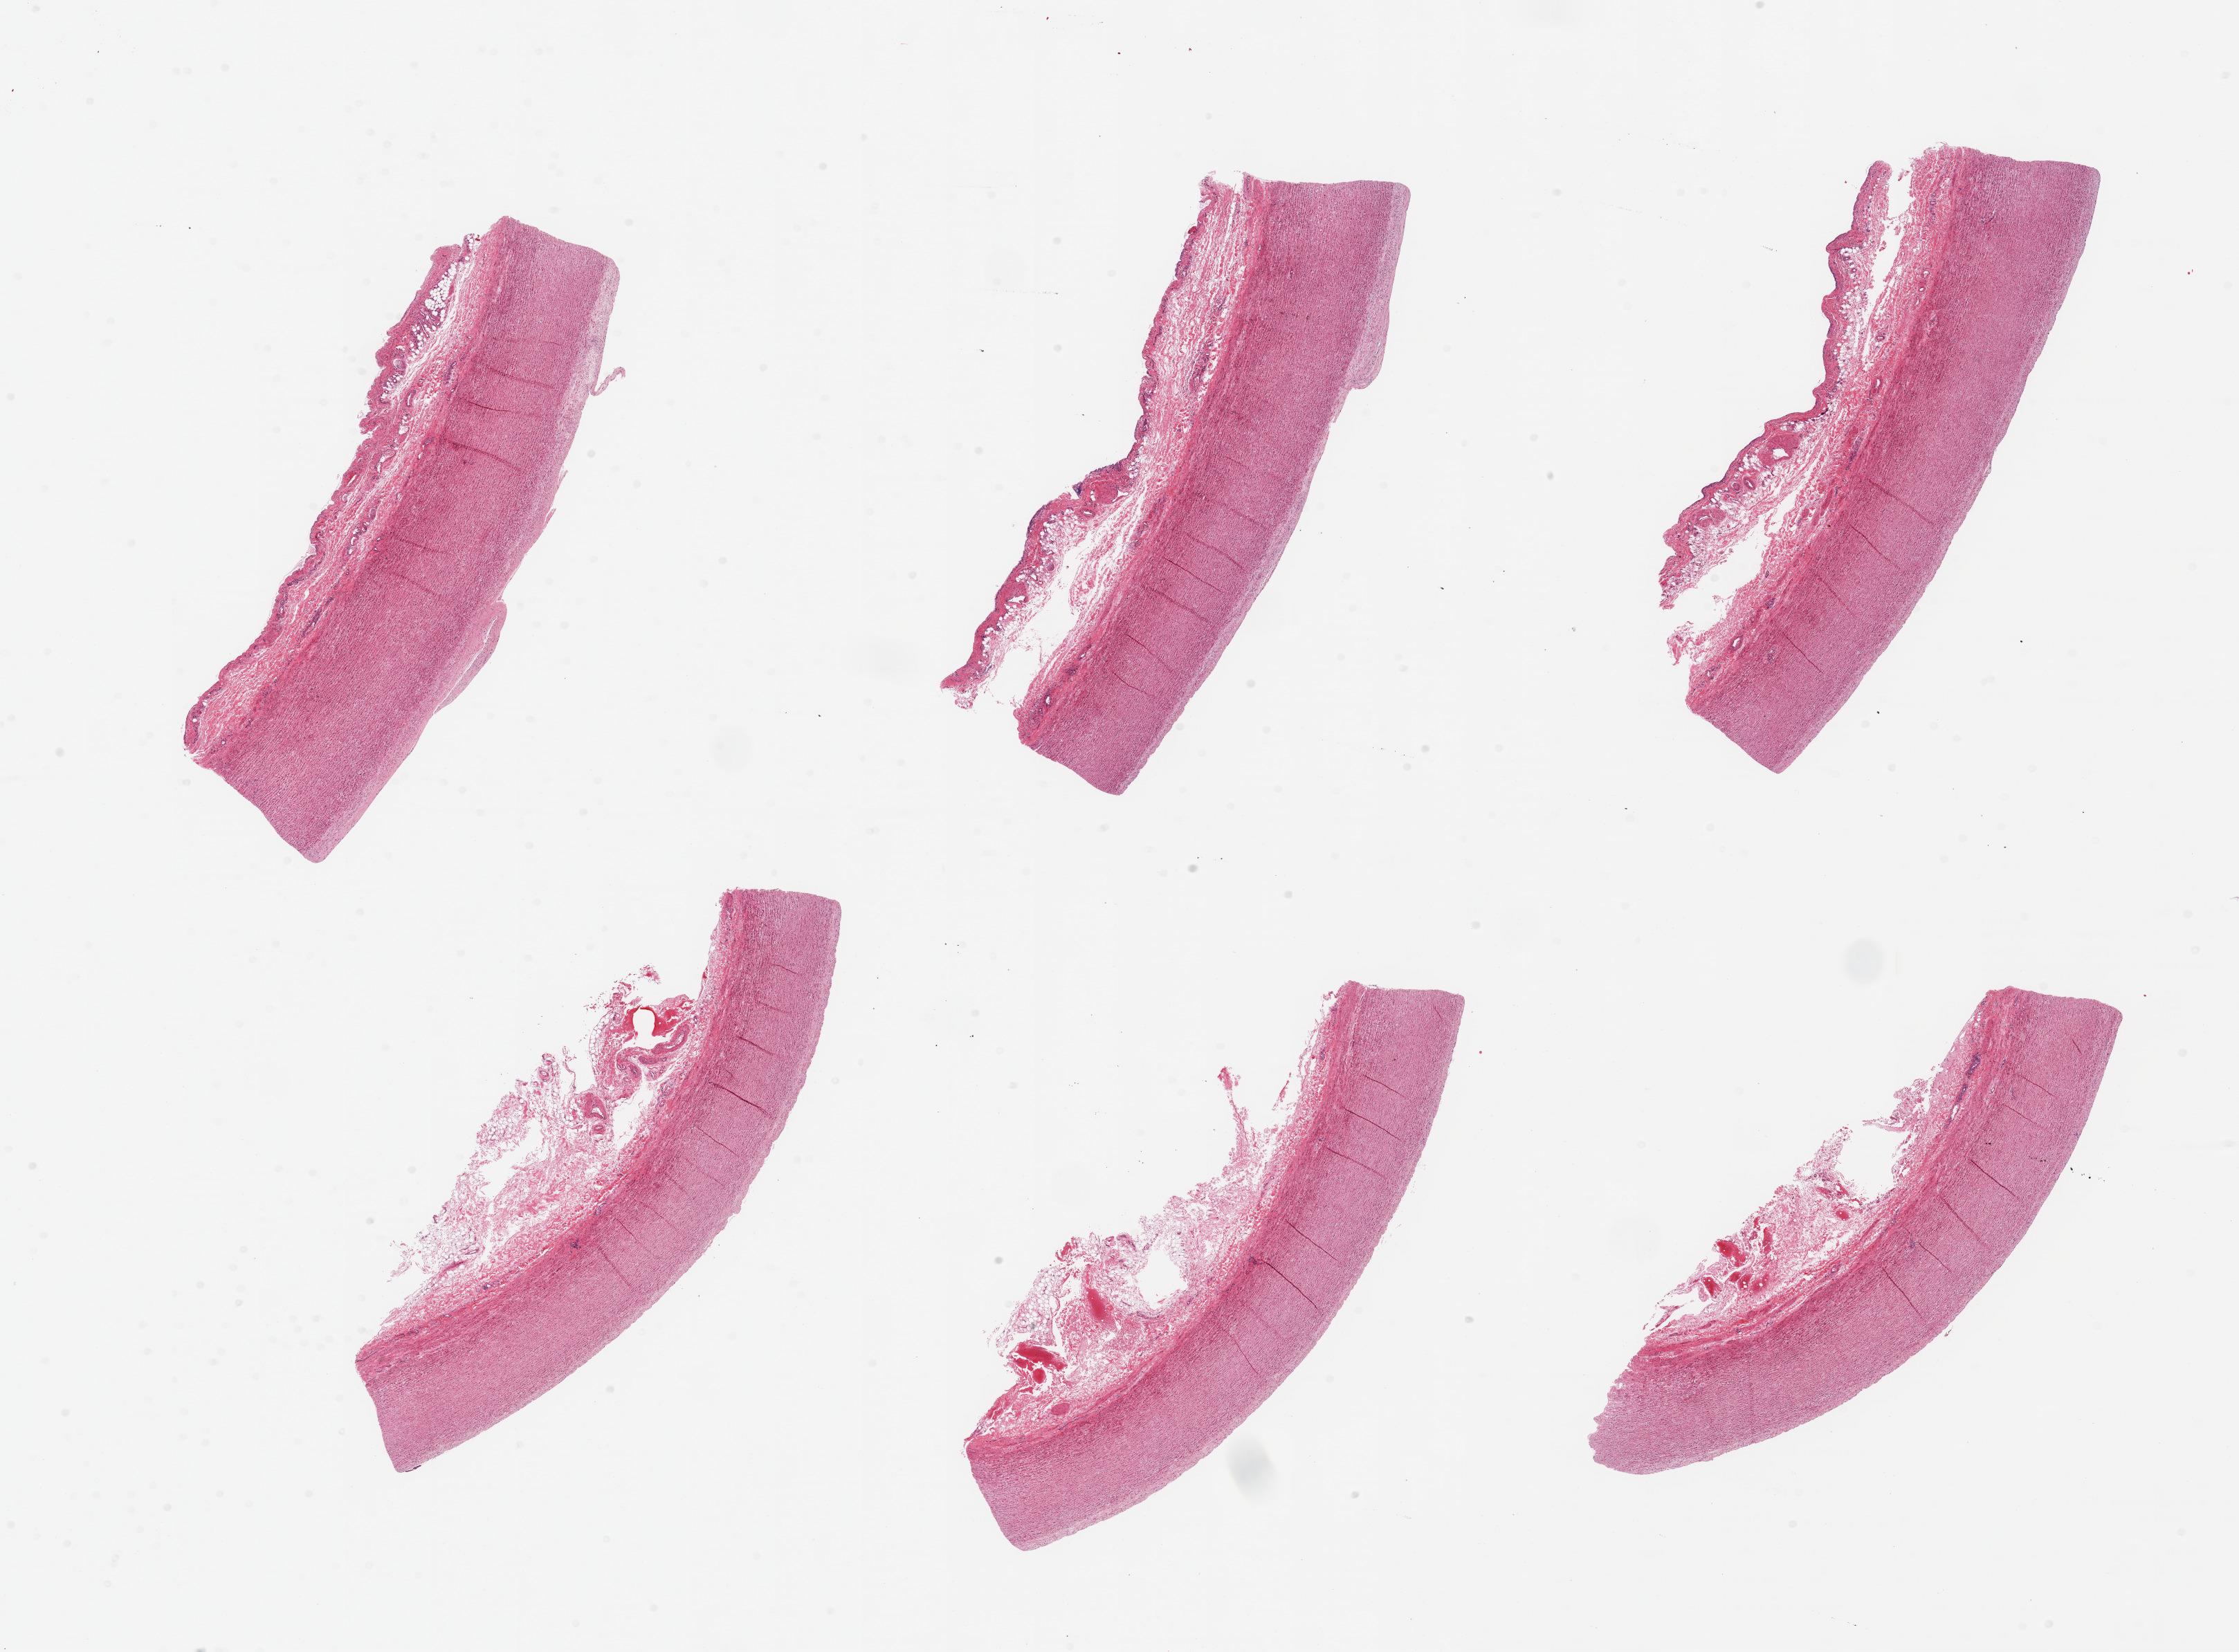
Digitized haematoxylin and eosin-stained section, brightfield — whole scanned area (about 25.6 x 18.9 mm, slide scanned at 20x) shown as a low-resolution overview; PAXgene-fixed paraffin-embedded (PFPE) section; section of aorta (target tissue); donor tissue sample.
Reviewer comment on this tissue sample: 6 pieces; minimal plaque; adventitia up to 1 mm thick.